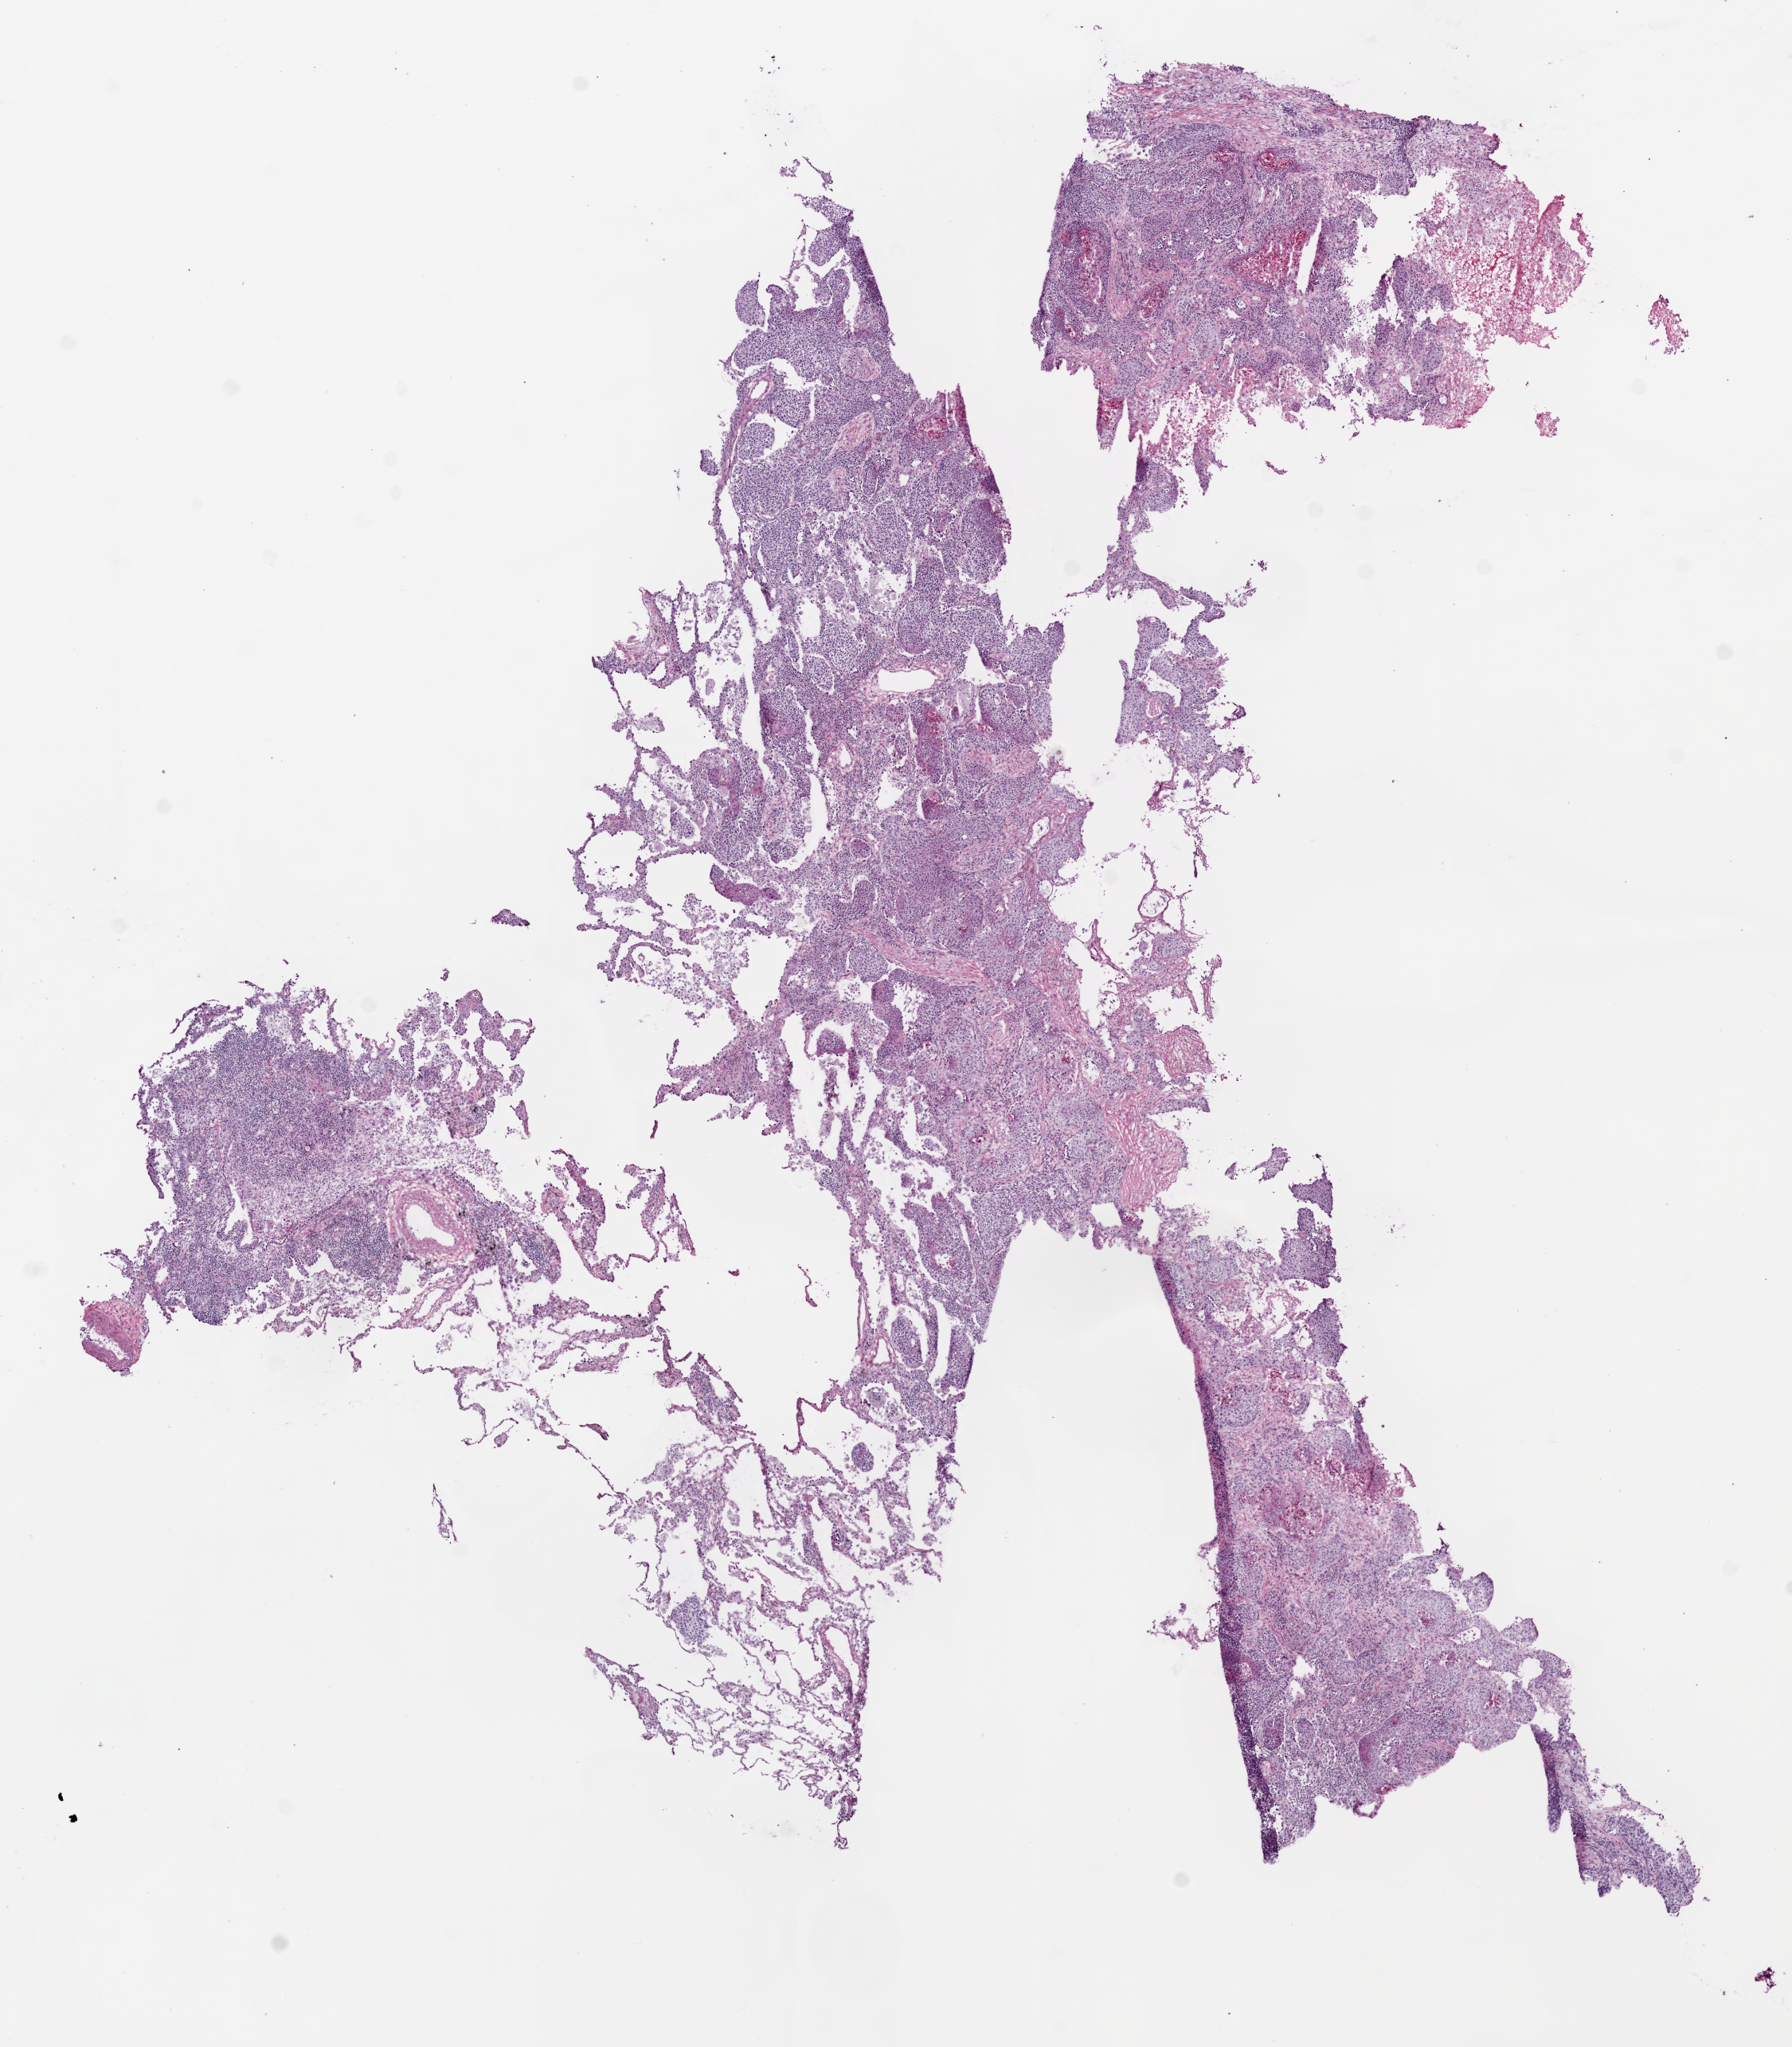
Hematoxylin and eosin (H&E) stained whole-slide image — shown as a low-resolution overview of the whole scanned area (about 9.0 x 10.3 mm); frozen section from the bottom of the tissue portion; lung, primary tumour sample. Patient: male, age at initial diagnosis 81 years. Composition of this section per pathologist review: tumour cells 60%, tumour nuclei 70%, normal cells 20%, stromal cells 10%, necrosis 10%.
AJCC pathologic stage: IA (6th edition). Diagnosis: Squamous cell carcinoma, NOS (upper lobe, lung). TNM: T1 N0 M0.